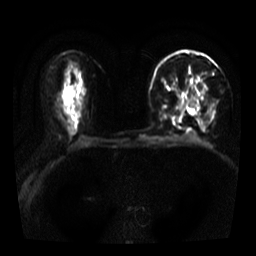
Breast MRI, one axial slice; position 20 of 39 along the scan axis; diffusion-weighted series; image 2 of 4 stored at this slice position (different b-values; order by instance number); 3 T; 5 mm slice thickness; 256 × 256 image matrix, field of view 320 × 320 mm. Female patient.
Annotated regions visible in this slice (expert manual segmentation):
- tumour on diffusion-weighted imaging: bounding box <193,82,197,87> (left, top, right, bottom; pixels)